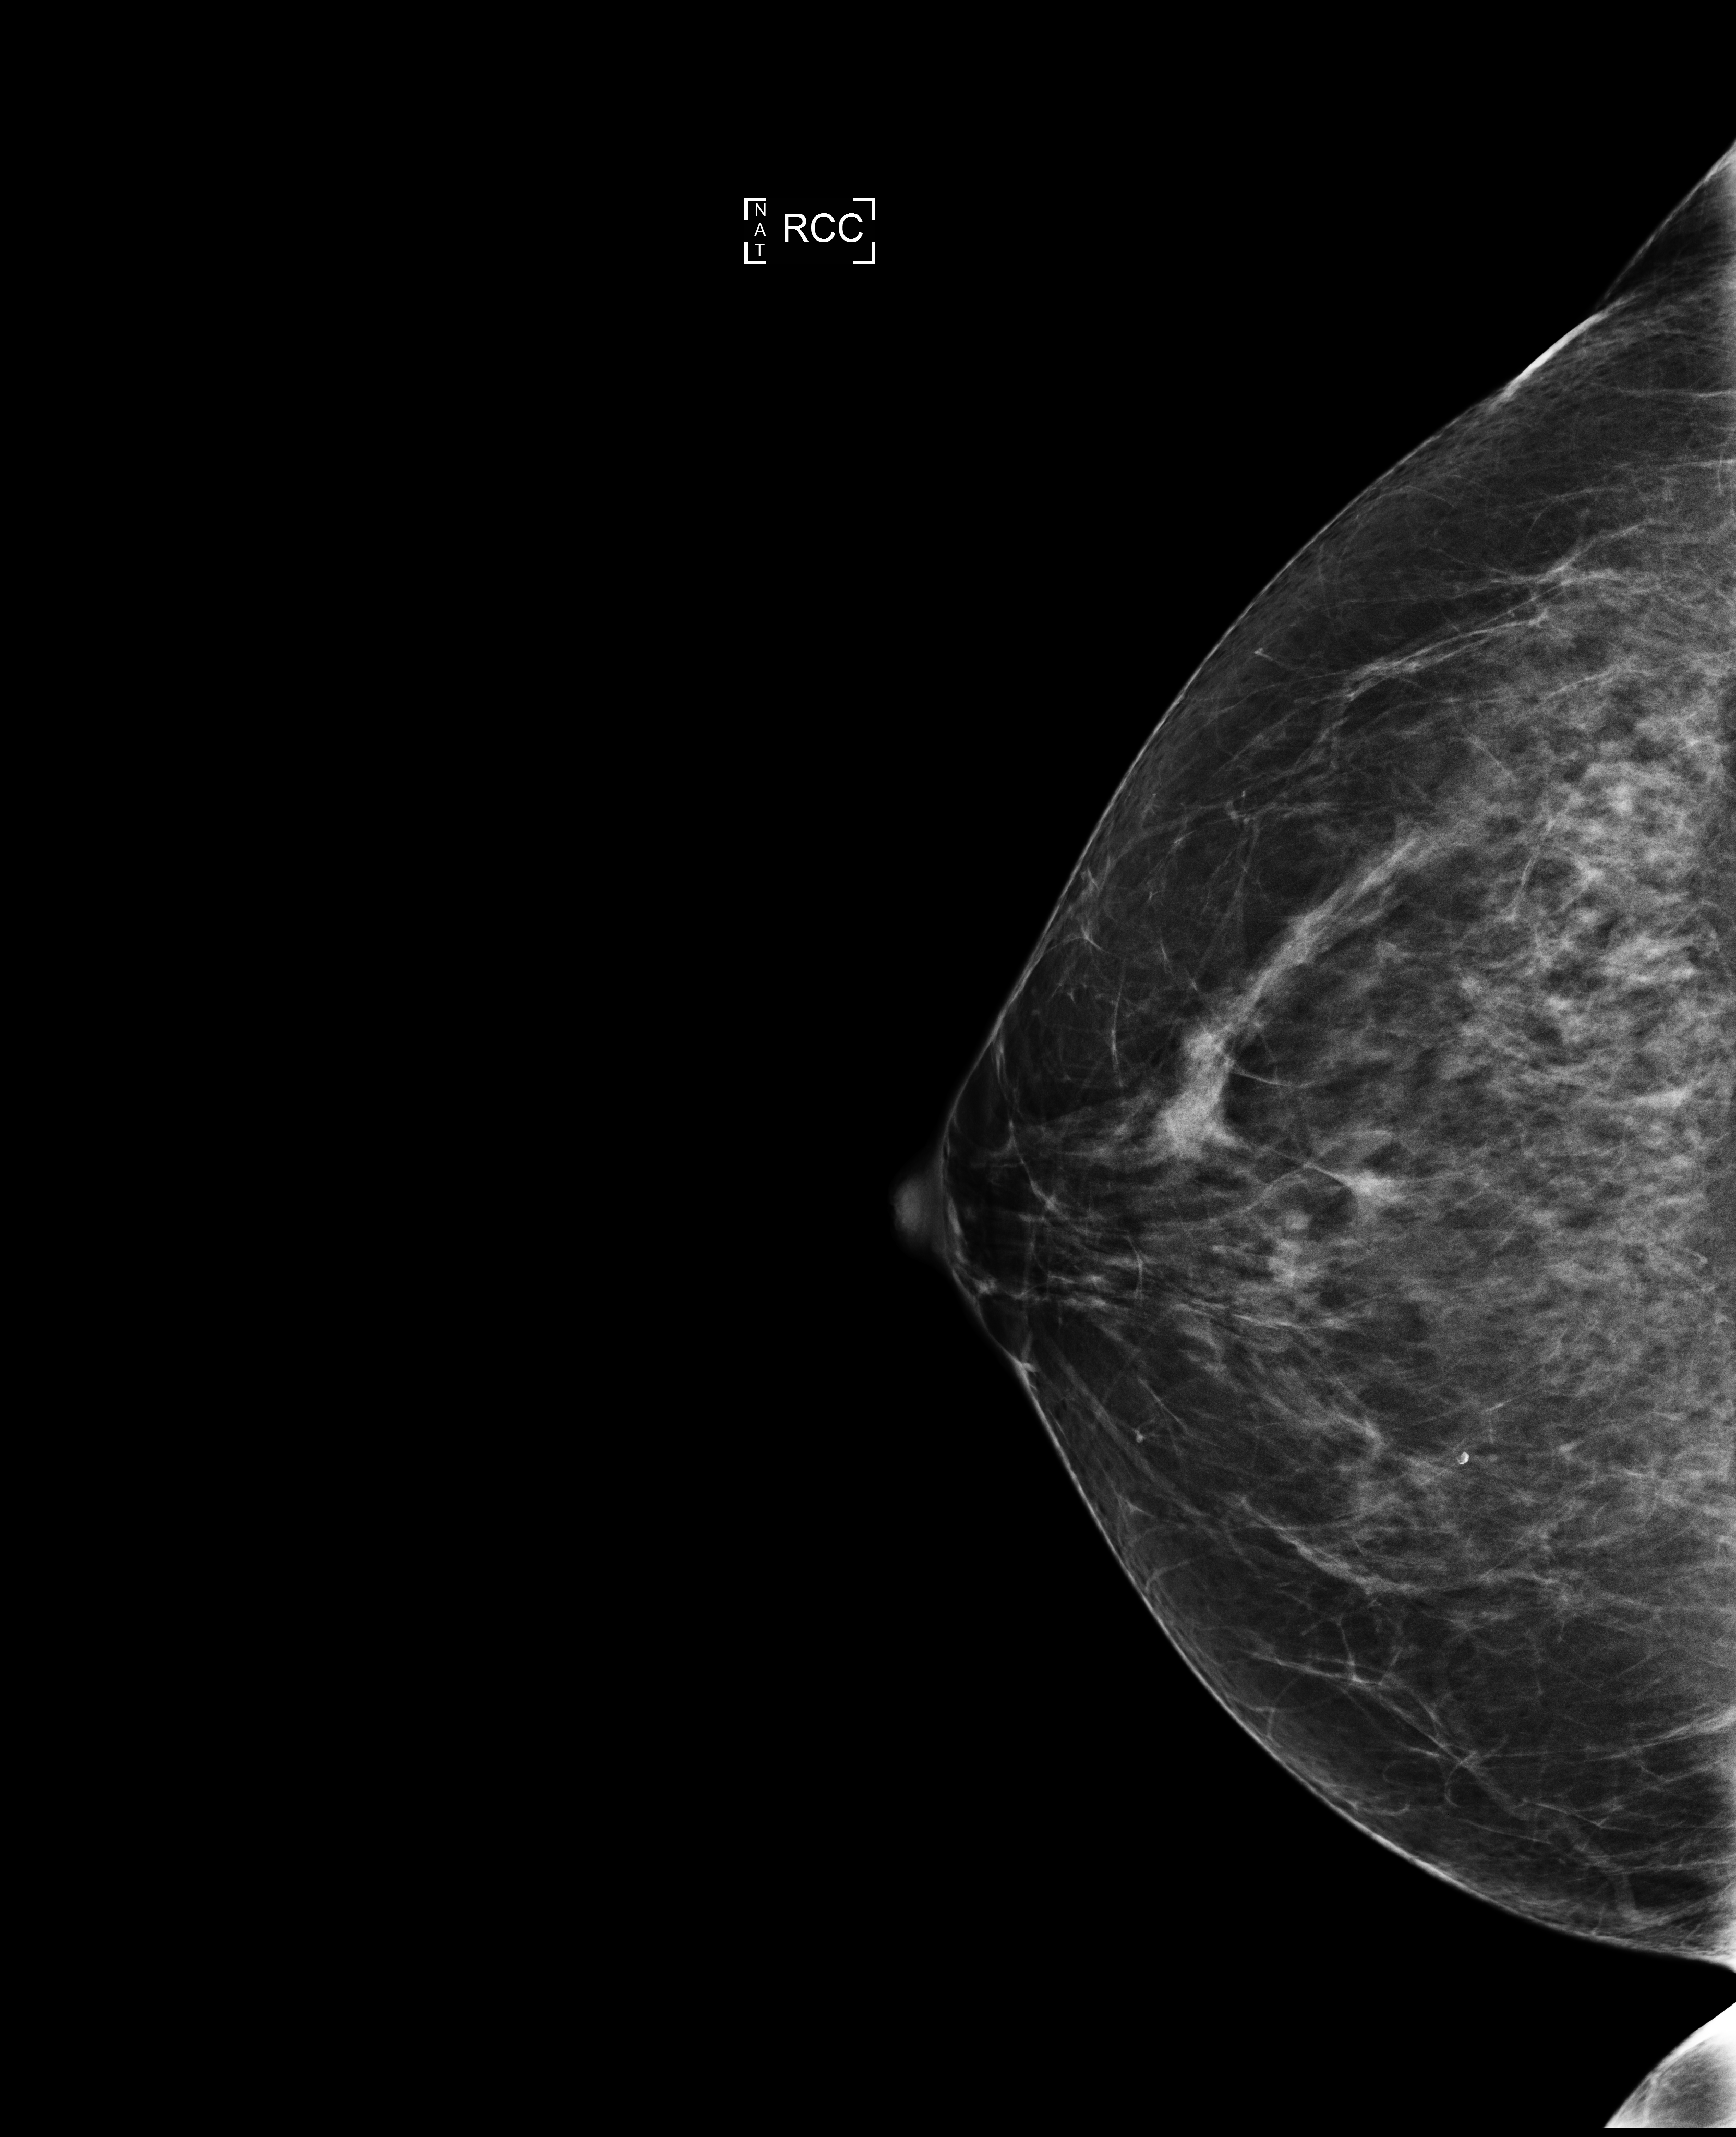
Digital mammogram (FFDM), right breast, CC view, screening examination, compressed breast thickness 85 mm, system: Selenia Dimensions. Patient: female, 52 years.
BI-RADS breast density category at the screening exam (both breasts, scale 1–4): 2. Final BI-RADS category for the screening round (tomosynthesis exam, both breasts): category 1. Recall: no recall after this screen.